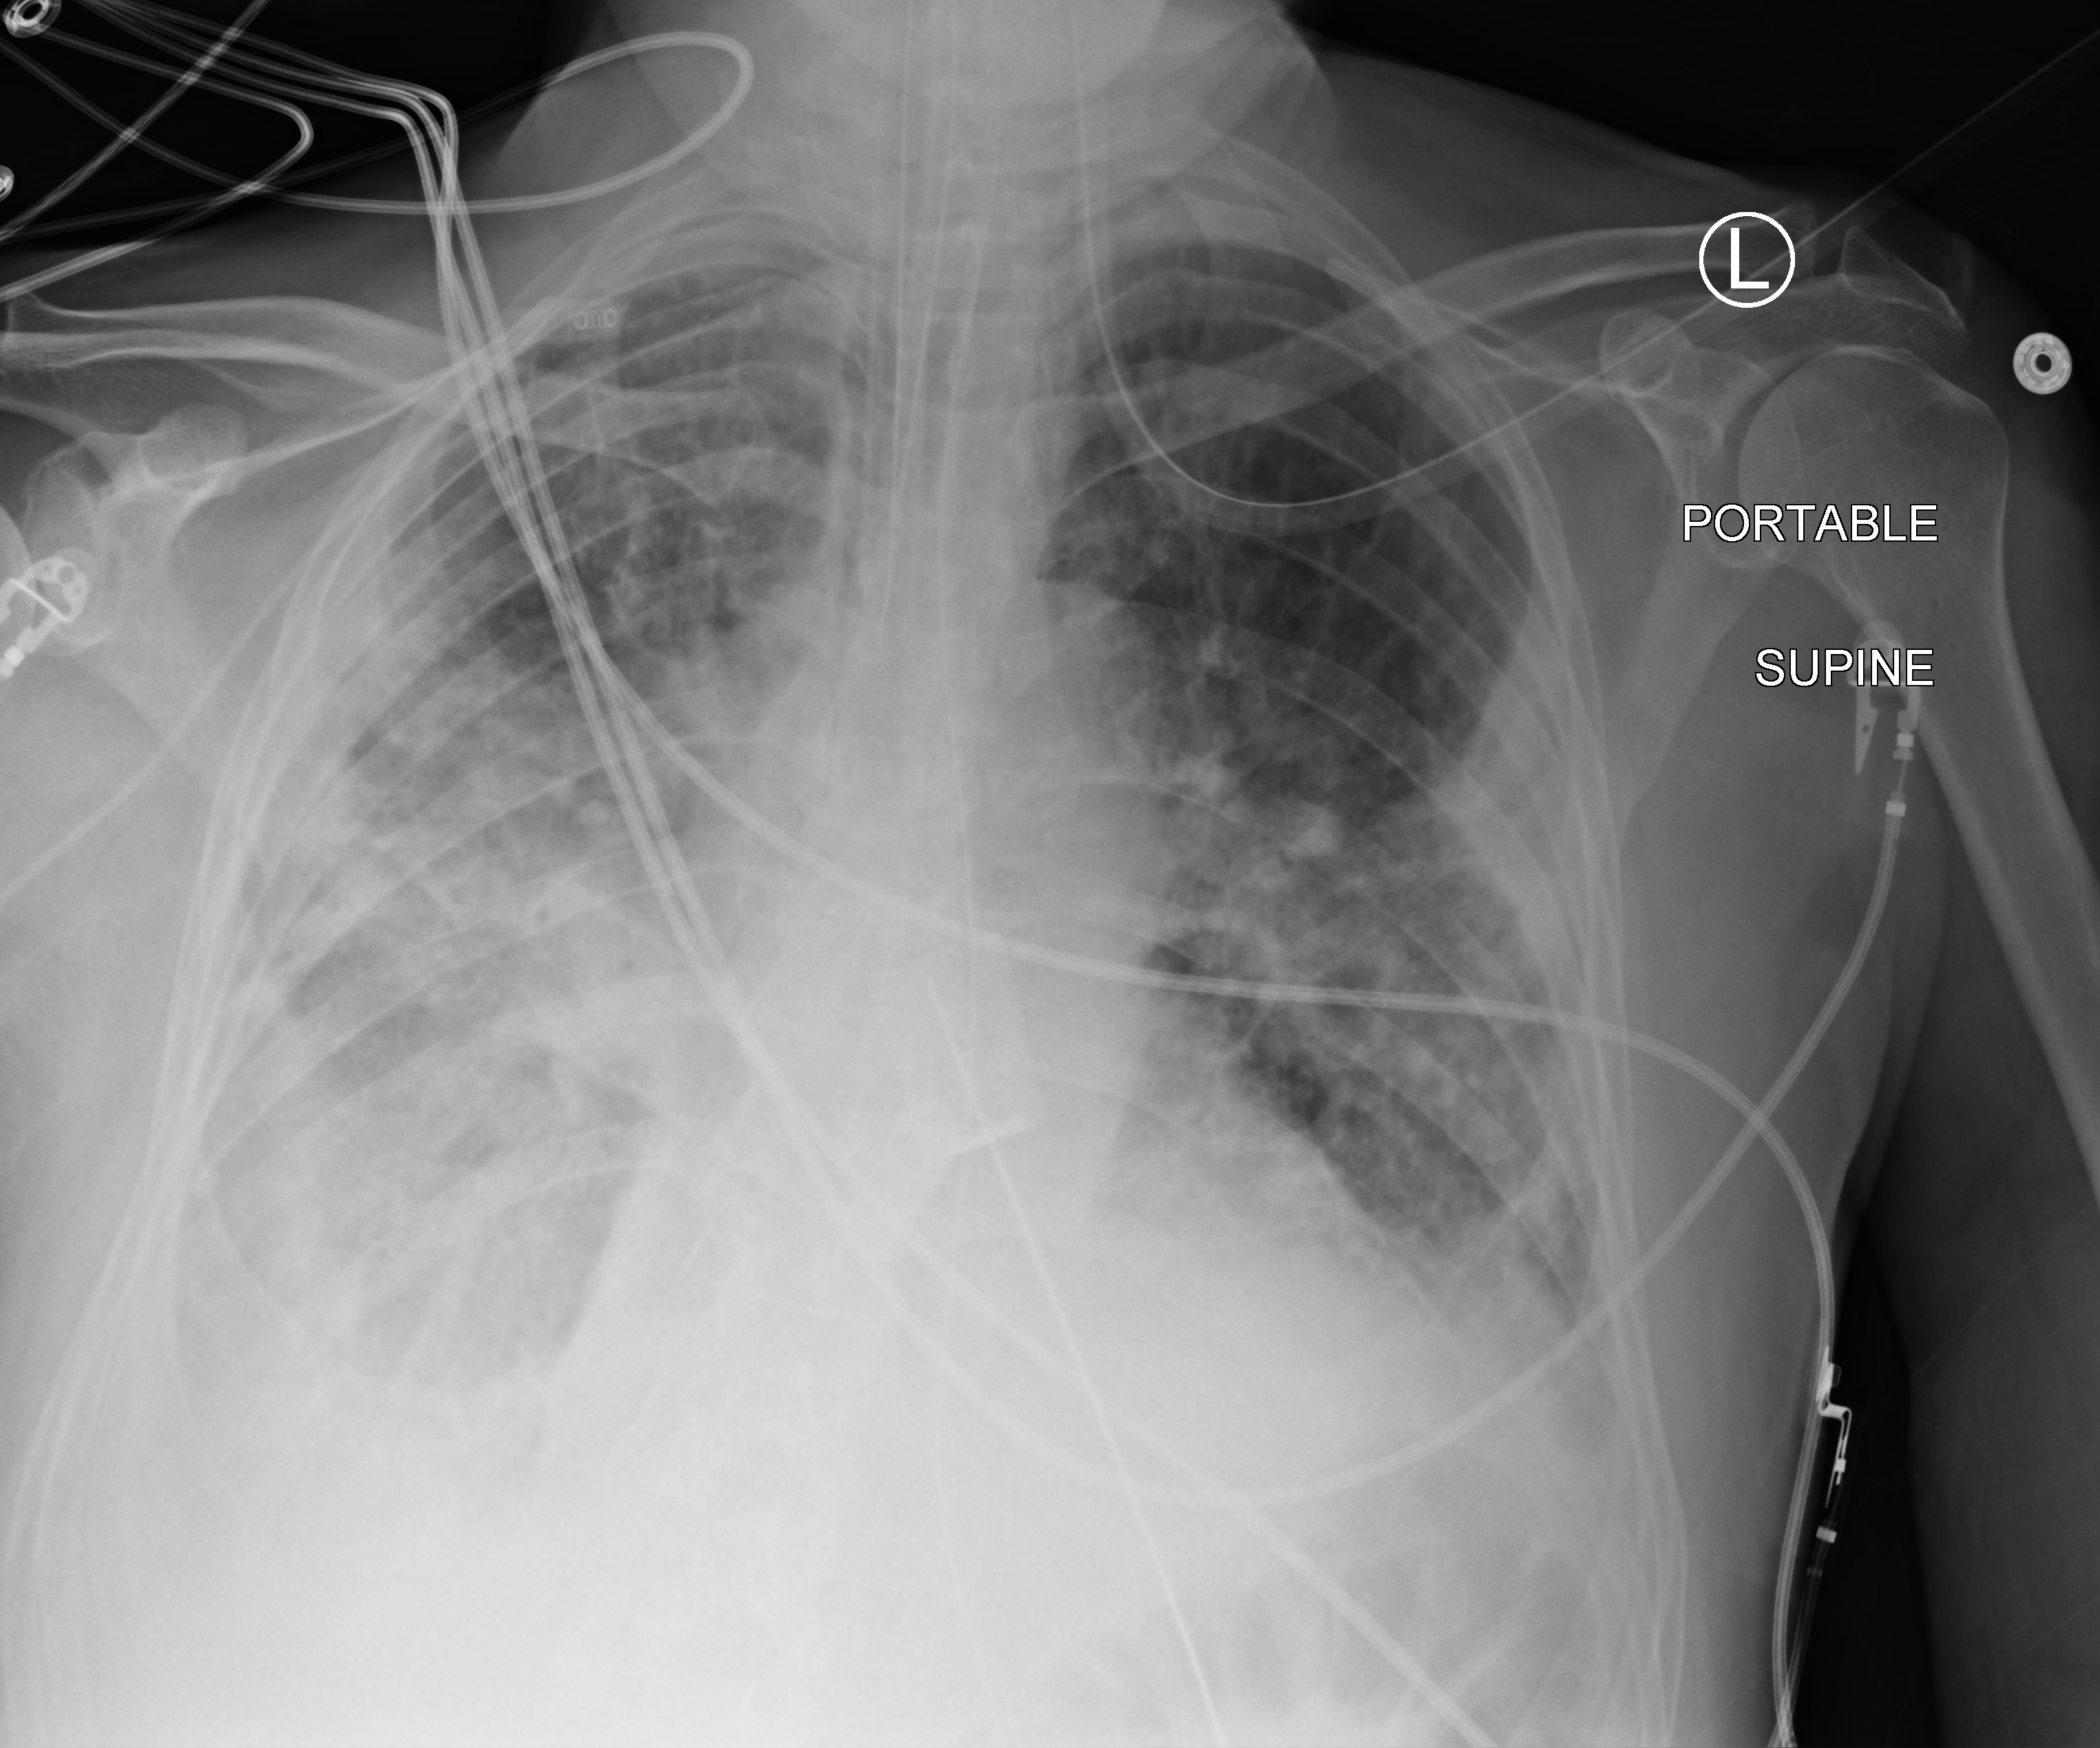
Bedside chest radiograph (computed radiography); anteroposterior (AP) projection. Patient hospitalised with COVID-19; male, aged 75–90 years.
Admission-level facts for this patient (not findings on this image; timing relative to this image not recorded): other chronic lung disease (admission record): yes; mechanically ventilated during this hospital stay: yes.